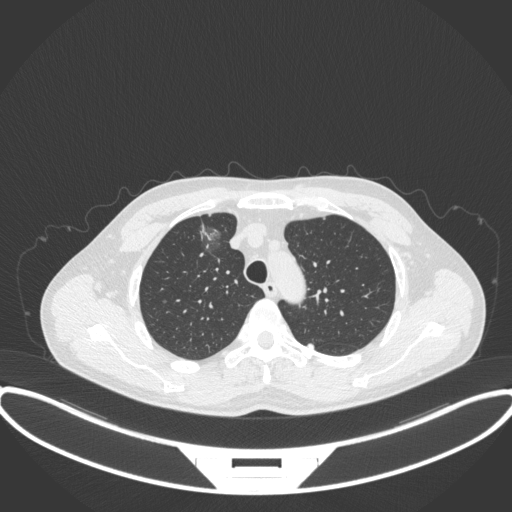
Chest CT, one axial slice; slice 284 of 395 in the series (ordered by position); reconstruction kernel B31f; 120 kVp; lung window (W 1500 / L -600 HU); 1 mm slice thickness; 512 × 512 image matrix. Male patient, age 60 years. Case-level facts recorded for this patient, not image findings: clinical TNM (as recorded): T1c N0 M0.
Annotated regions visible in this slice (bounding box drawn by a radiologist):
- lung tumour (recorded histology: adenocarcinoma): bounding box [x1, y1, x2, y2] px = [194, 217, 225, 260]